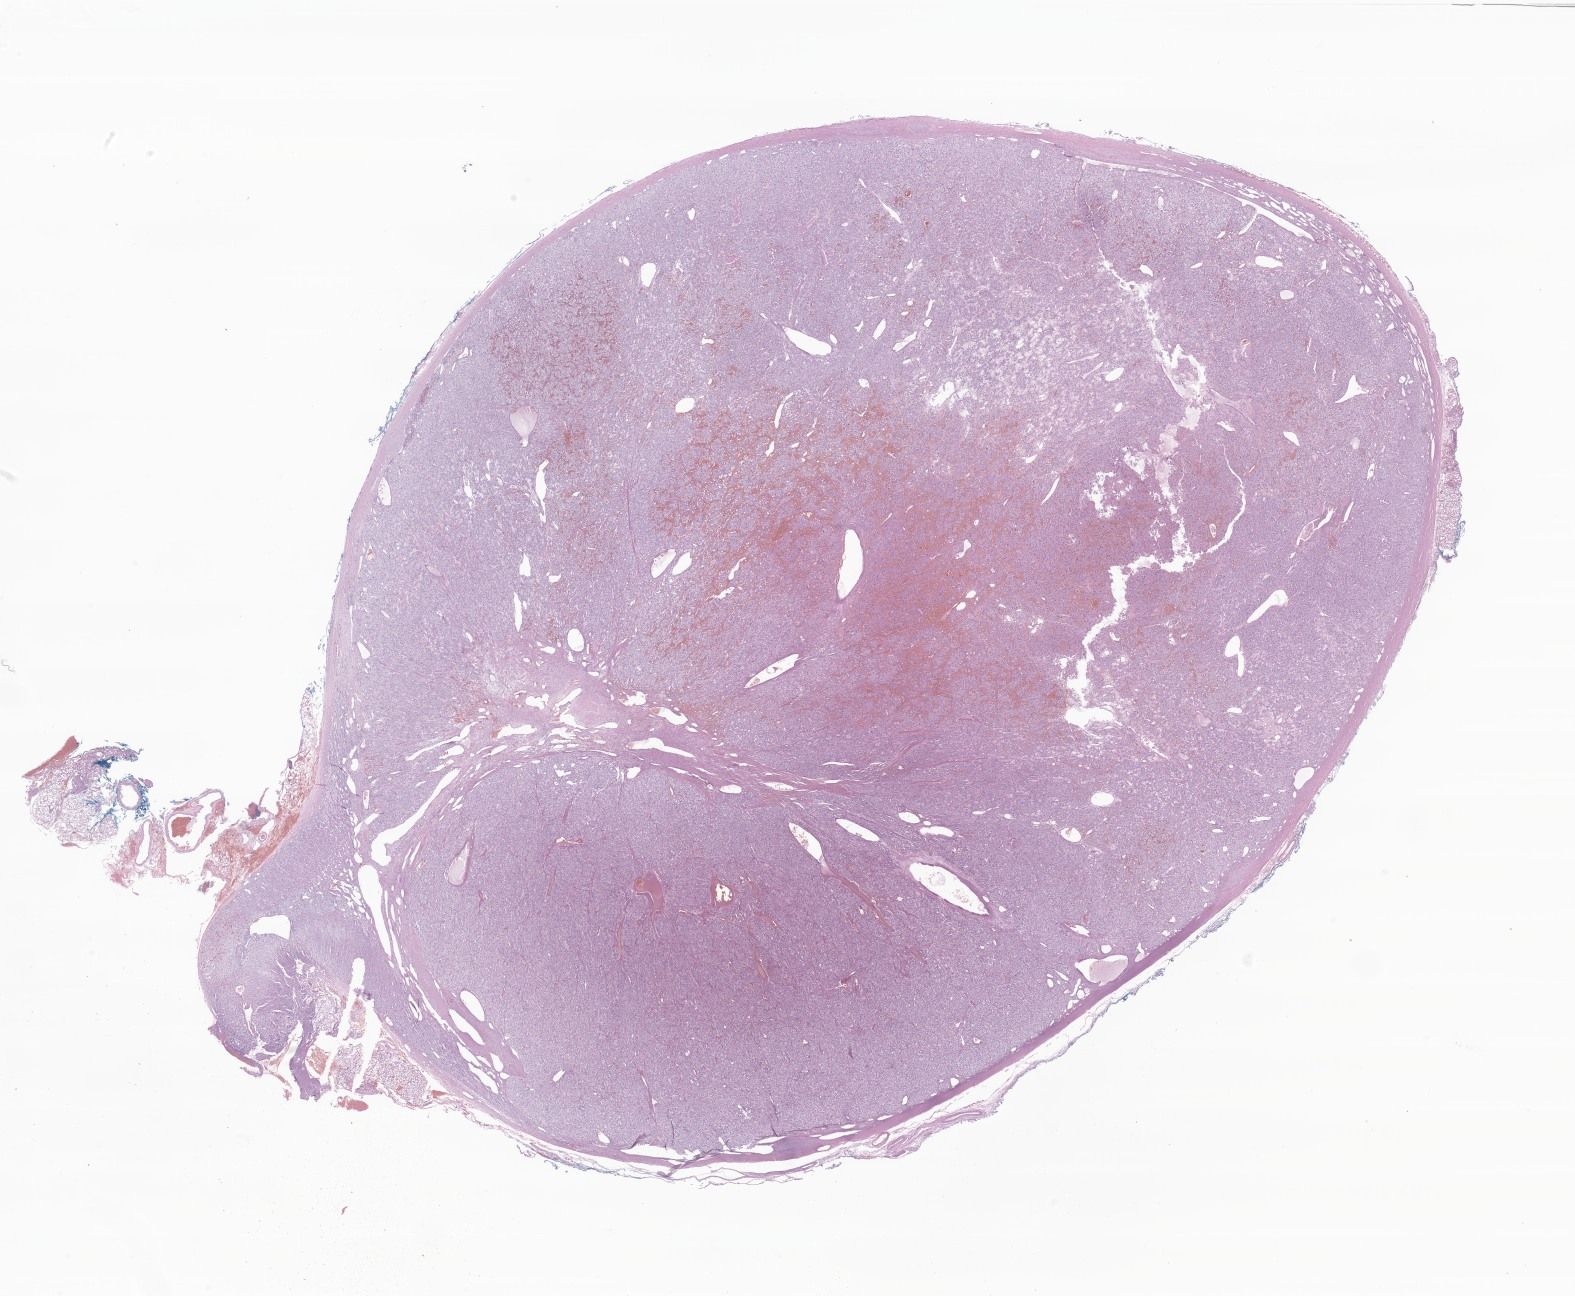
Whole-slide image, H&E stain of tumor tissue from the adrenal gland — shown as a low-resolution overview of the whole scanned area (about 26.6 x 21.9 mm). Formalin-fixed paraffin-embedded section. Patient: male, age 185 months (15 years 5 months).
Recorded diagnosis: Pheochromocytoma, NOS.